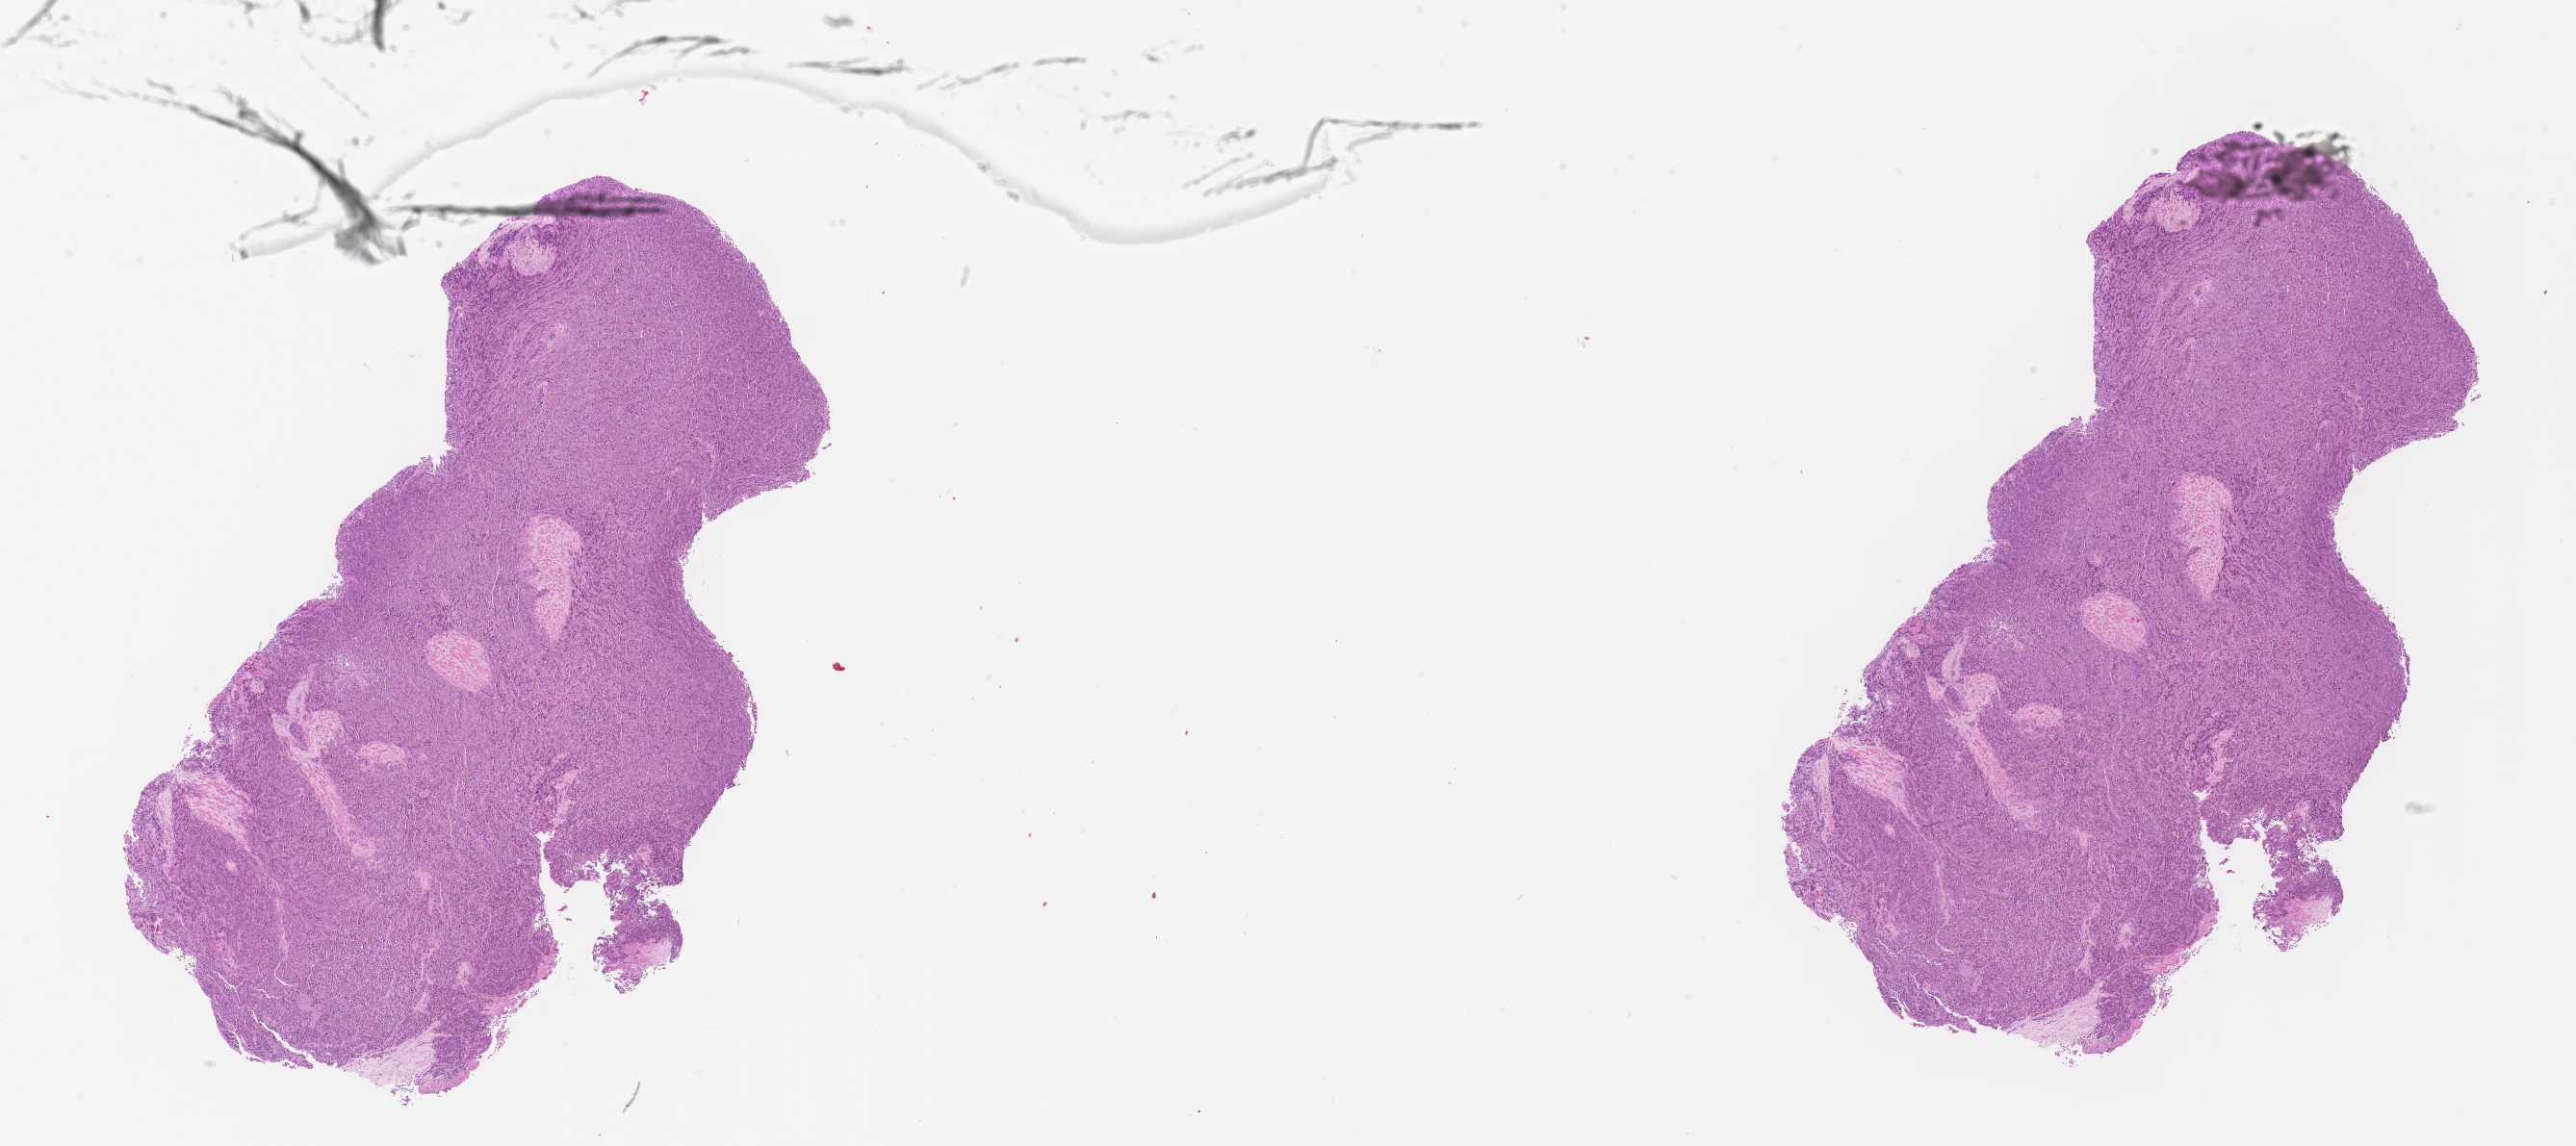
Whole-slide image, haematoxylin and eosin stain of tumor tissue, low-resolution overview of the scanned area, about 21.6 x 9.6 mm; formalin-fixed paraffin-embedded section; sample anatomic site: soft tissue, forearm-left. Patient: male, age 1.7 years at diagnosis.
Diagnosis: rhabdomyosarcoma; histological classification: alveolar rhabdomyosarcoma.